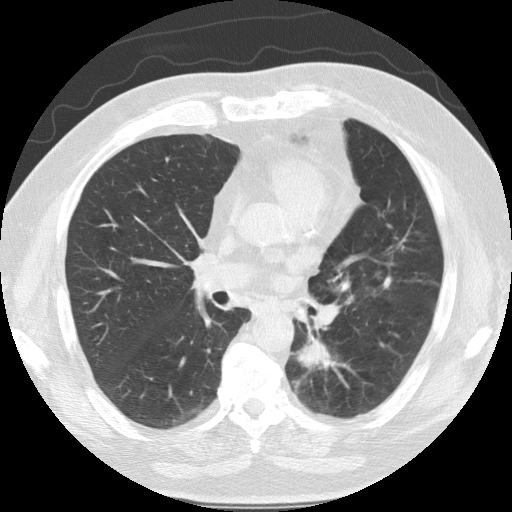
Low-dose screening chest CT, one axial slice; slice 65 of 124 in the series (ordered by position); lung window (W 1500 / L -600 HU); 2.5 mm slice thickness; 512 × 512 image matrix, field of view 360 × 360 mm.
Annotated regions visible in this slice (manually delineated by an expert):
- lesion 1 (tumor, lower lobe of left lung): bounding box <291,338,334,371> (left, top, right, bottom; pixels)